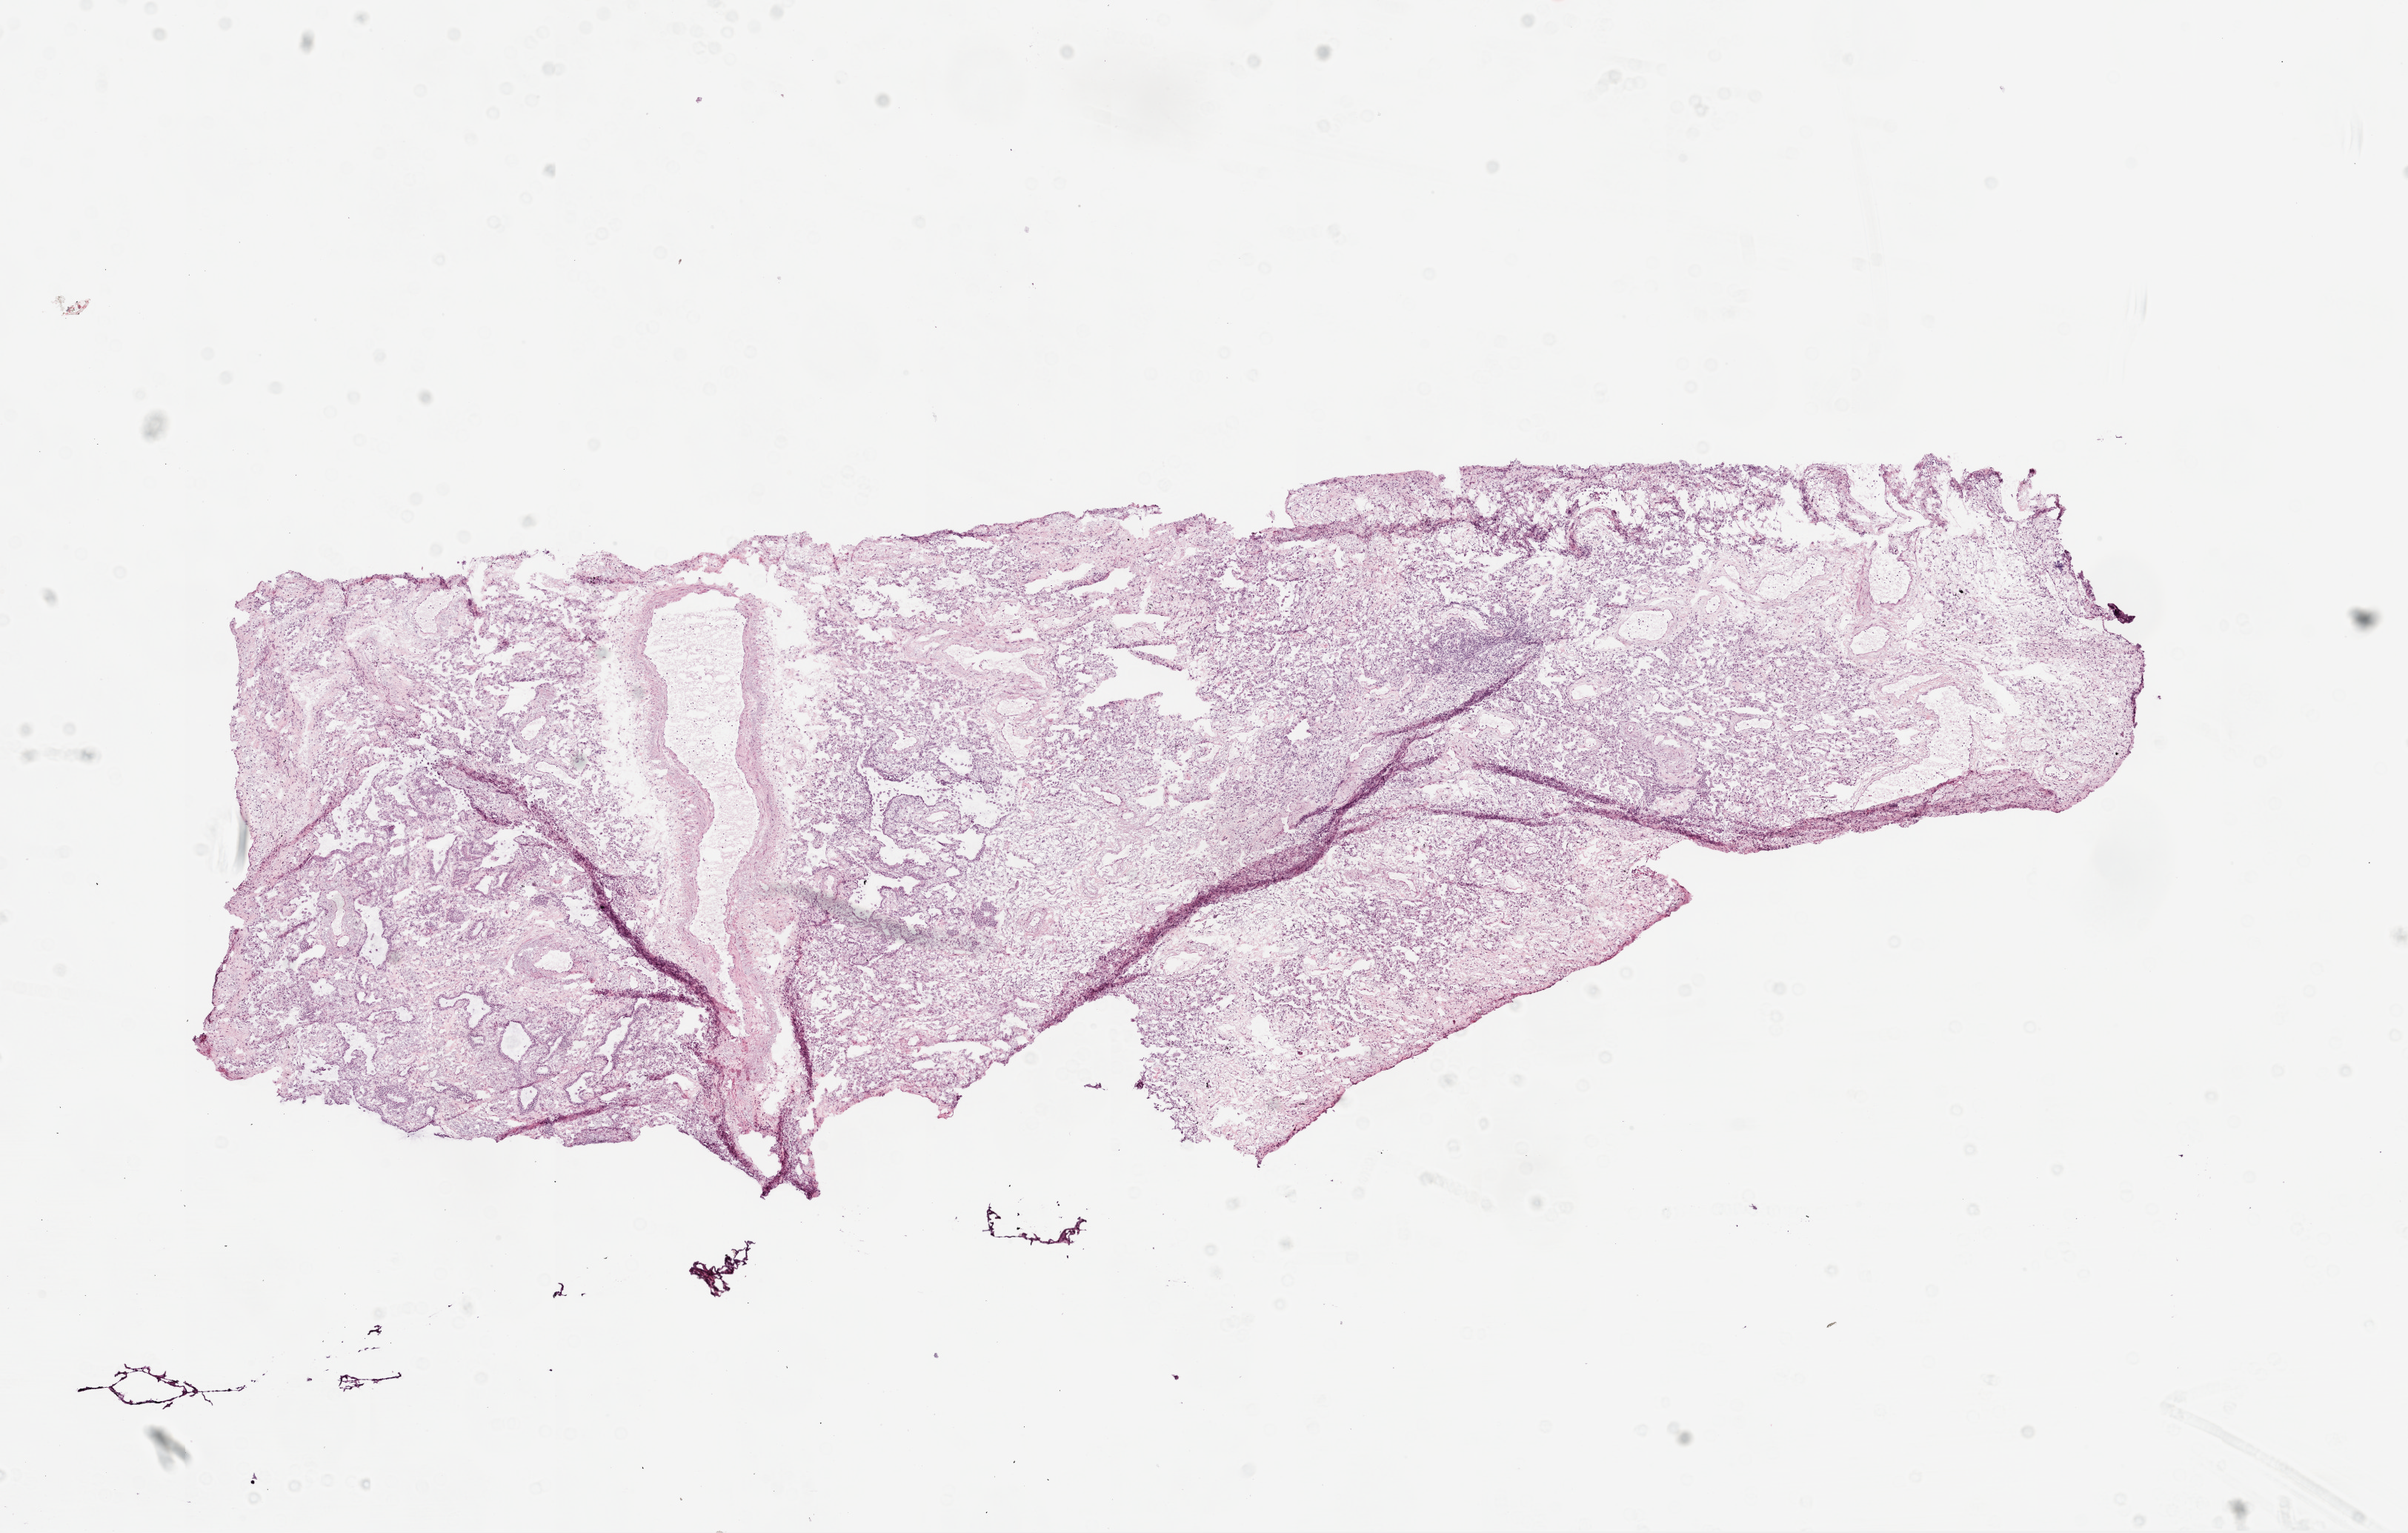
Whole-slide histology image, H&E-stained, shown as a low-resolution overview of the whole scanned area (about 13.0 x 8.3 mm, acquisition: 20x scan), frozen section from the top of the tissue portion, lung, solid tissue normal (non-tumour tissue) sample. Patient: female, age at initial diagnosis 74 years.
This section: solid tissue normal sample (biorepository sample class). Patient diagnosis: Basaloid squamous cell carcinoma (upper lobe, lung).